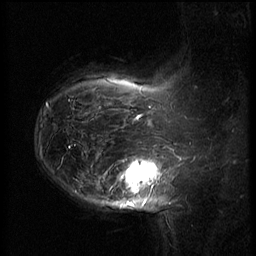
Breast MRI (dynamic contrast-enhanced), one sagittal slice. Position 48 of 62 along the scan axis. 3 images stored at this slice position (order not interpretable as contrast timing). 1.5 T. TE 4.2 ms, TR 8.9 ms. 256 × 256 image matrix. Patient: female, 37 years. Case-level facts recorded for this patient, not image findings: setting: breast cancer imaged before/during neoadjuvant chemotherapy; receptor status: triple-negative.
Structures marked on this image (semi-automatically segmented with operator editing):
- analysis volume of interest (the breast-tissue region the enhancement analysis was run in; not a lesion): bounding box (x1, y1, x2, y2) in pixels: (116, 146, 168, 203)
- tumour enhancement mask (voxels above the 140 % enhancement threshold inside the analysis volume of interest): (121, 160, 165, 191)